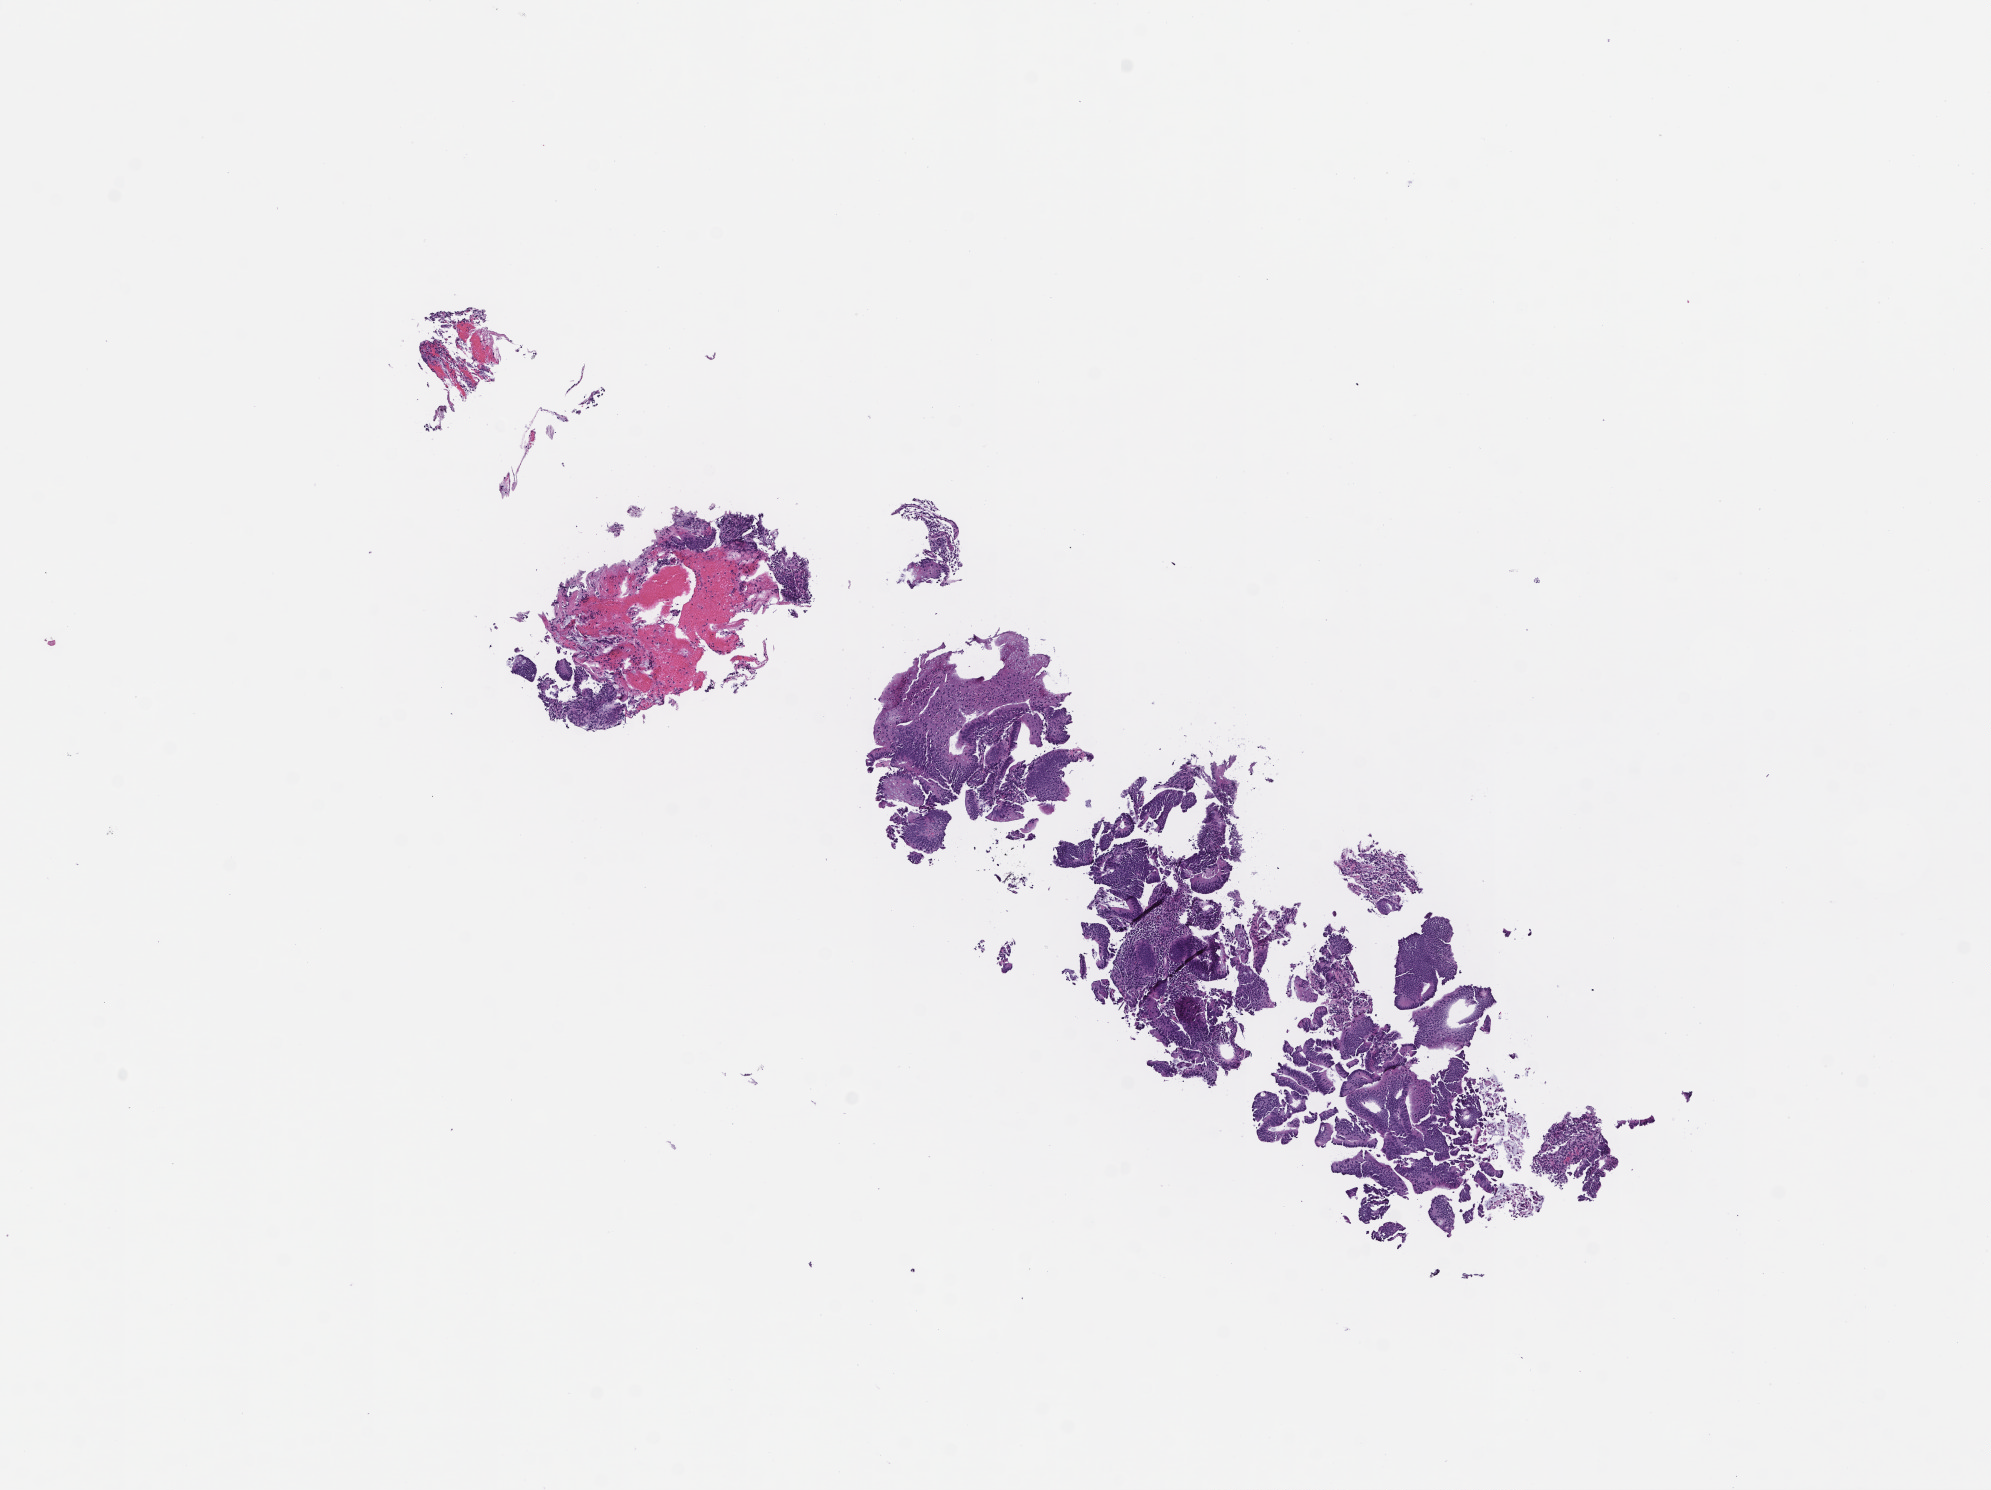
Hematoxylin and eosin (H&E) whole-slide image, low-resolution overview of the scanned area, about 8.0 x 6.0 mm, FFPE section. Patient sex: male.
This section: metastatic tumor tissue. Primary diagnosis of the patient: Colorectal Carcinoma.